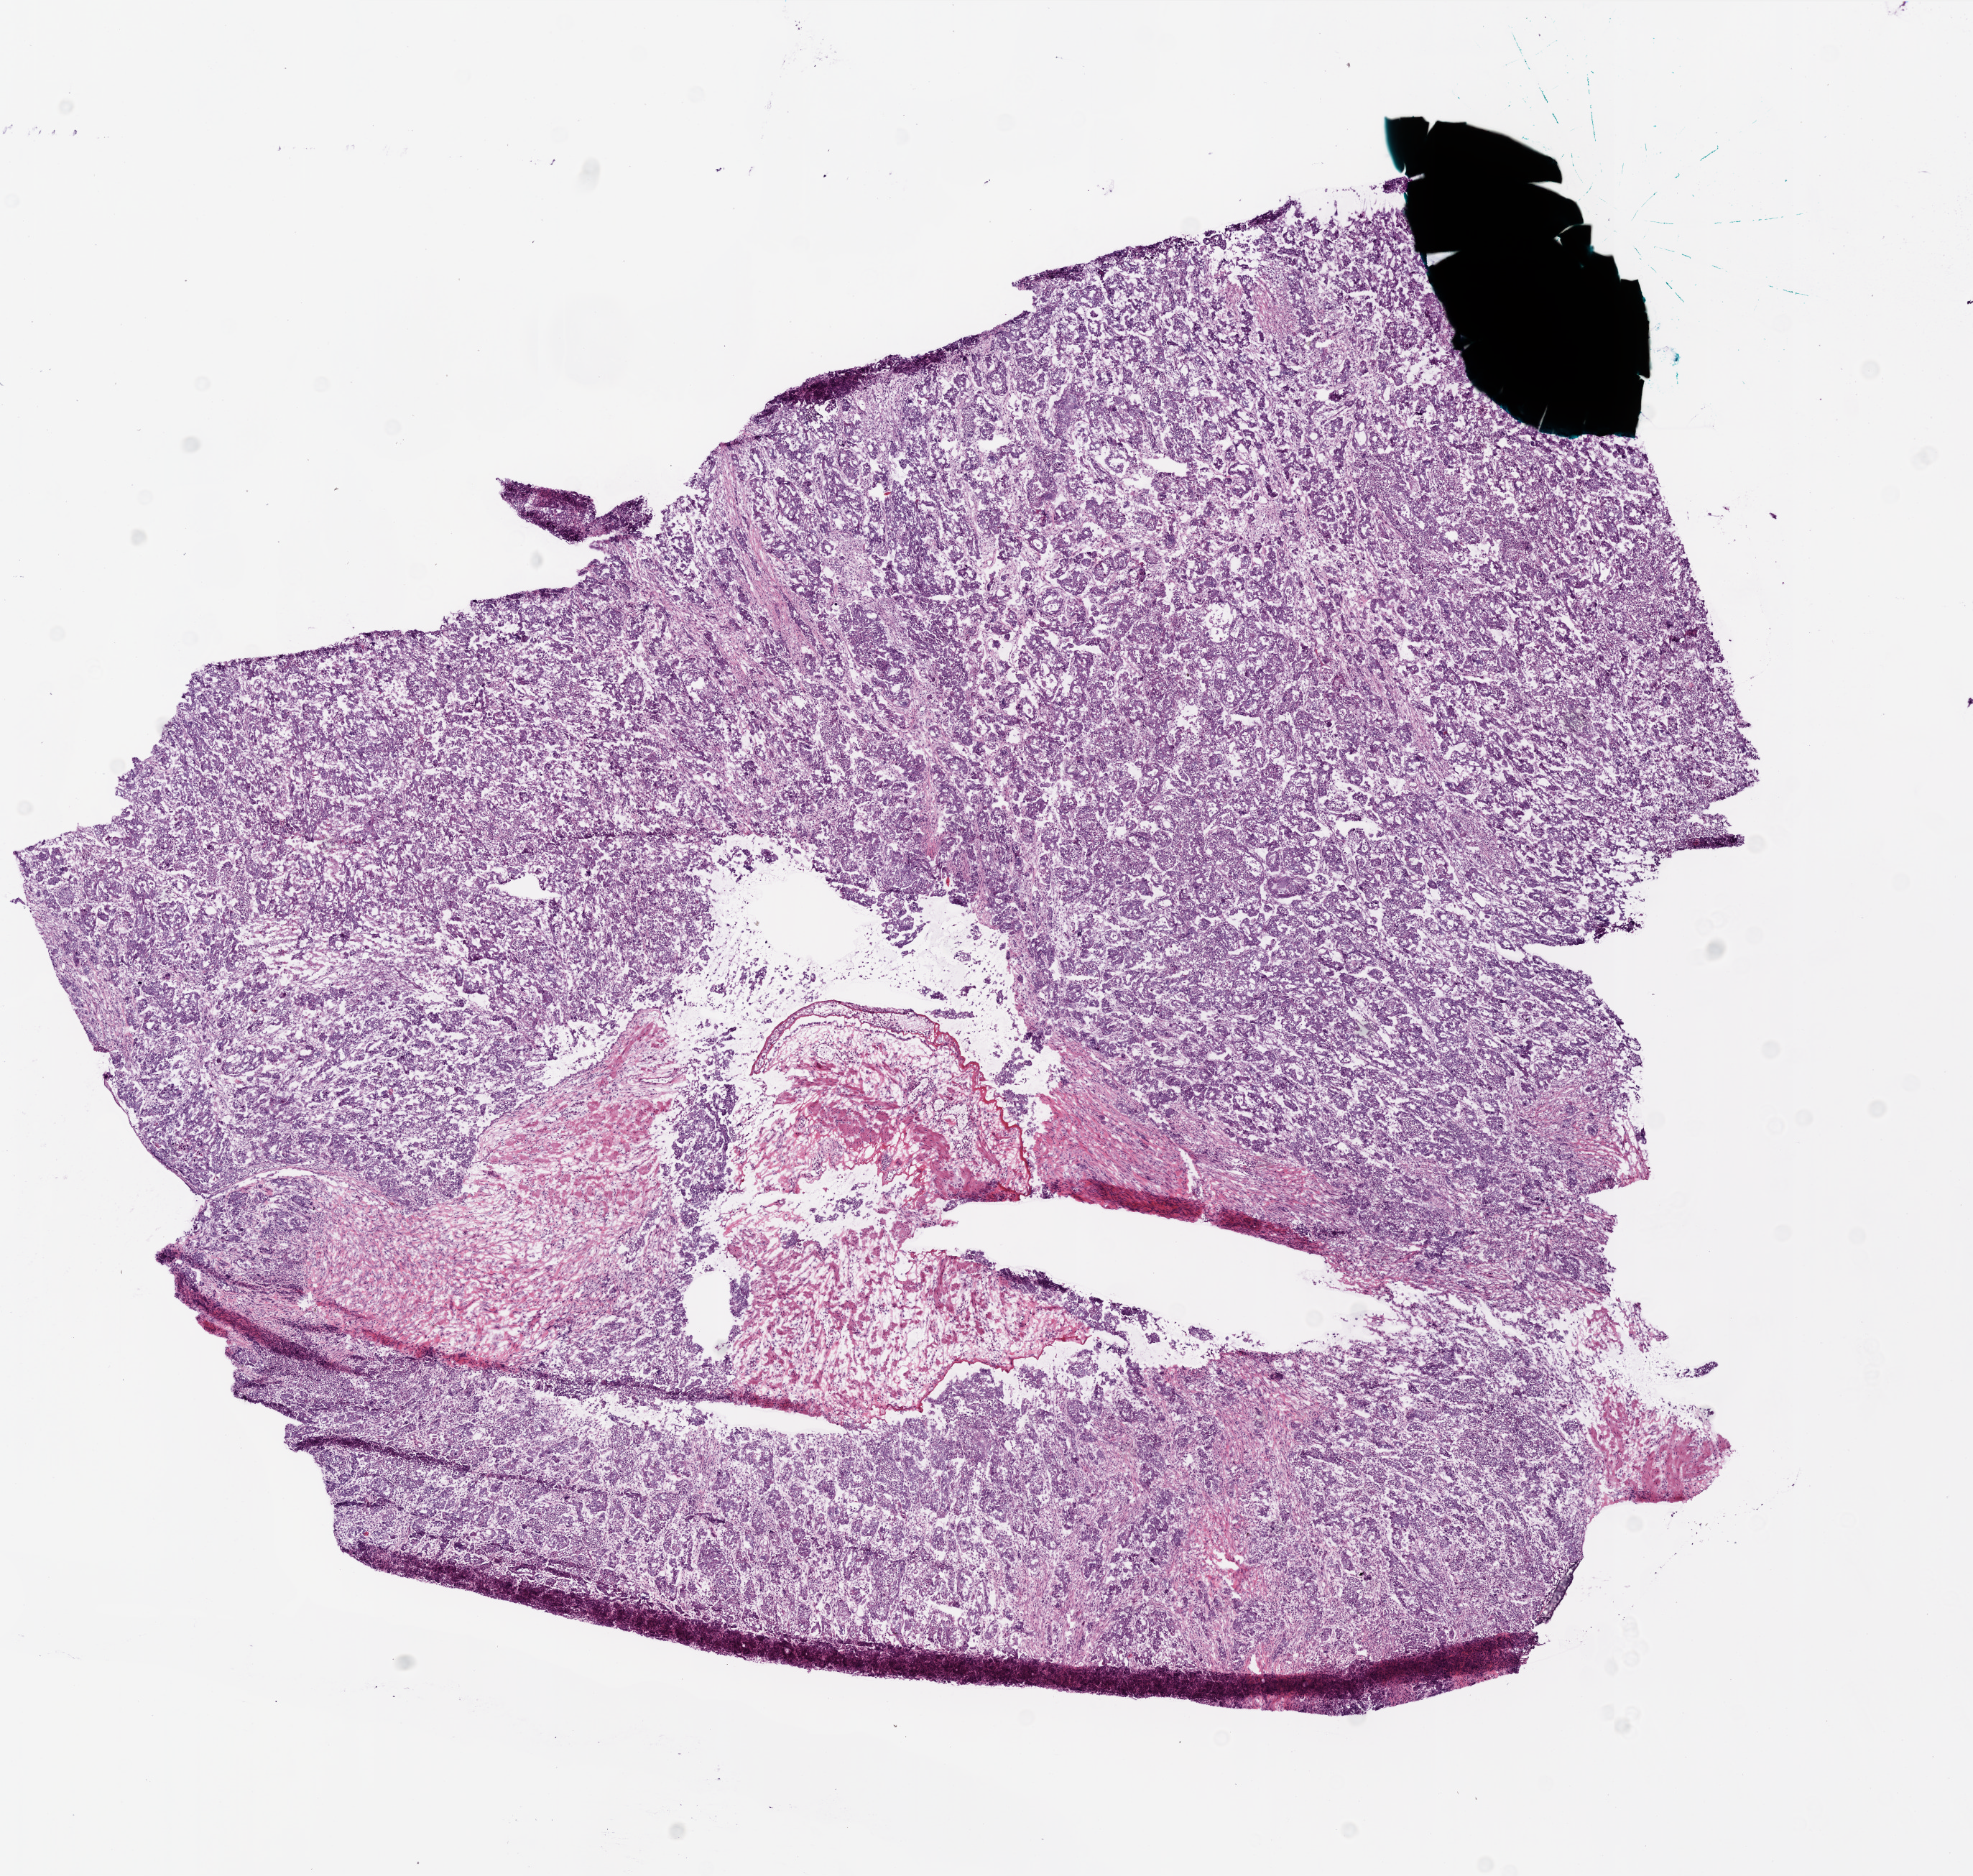
Whole-slide histology image, Hematoxylin and eosin (H&E) stained — whole scanned area (about 11.0 x 10.4 mm) shown as a low-resolution overview; frozen section from the bottom of the tissue portion; sample: primary tumour, ovary. Female, age 83 years at initial diagnosis. Histologic grade: G3 (poorly differentiated). Composition of this section per pathologist review: tumour nuclei 90%, normal cells 0%, necrosis 5%.
- laterality: left
- FIGO stage: IIIC
- histologic diagnosis: Serous cystadenocarcinoma, NOS